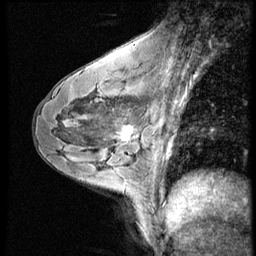
Breast MRI (dynamic contrast-enhanced), one sagittal slice; slice 36 of 56 in the series (ordered by position); dynamic contrast-enhanced series, image 2 of 4 at this slice position (ordered by acquisition); 1.5 T; TE 4.2 ms, TR 9 ms; 2.5 mm slice thickness; 256 × 256 image matrix, field of view 180 × 180 mm. Patient: female, 43 years. Case-level facts recorded for this patient, not image findings: setting: breast cancer imaged before/during neoadjuvant chemotherapy; receptor status: HR-positive, HER2-negative.
Structures marked on this image (semi-automatic segmentation, software-assisted and operator-edited):
- analysis volume of interest (the breast-tissue region the enhancement analysis was run in; not a lesion): bounding box [x1, y1, x2, y2] px = [104, 104, 152, 159]
- tumour enhancement mask (voxels above the 140 % enhancement threshold inside the analysis volume of interest): [123, 126, 133, 141]